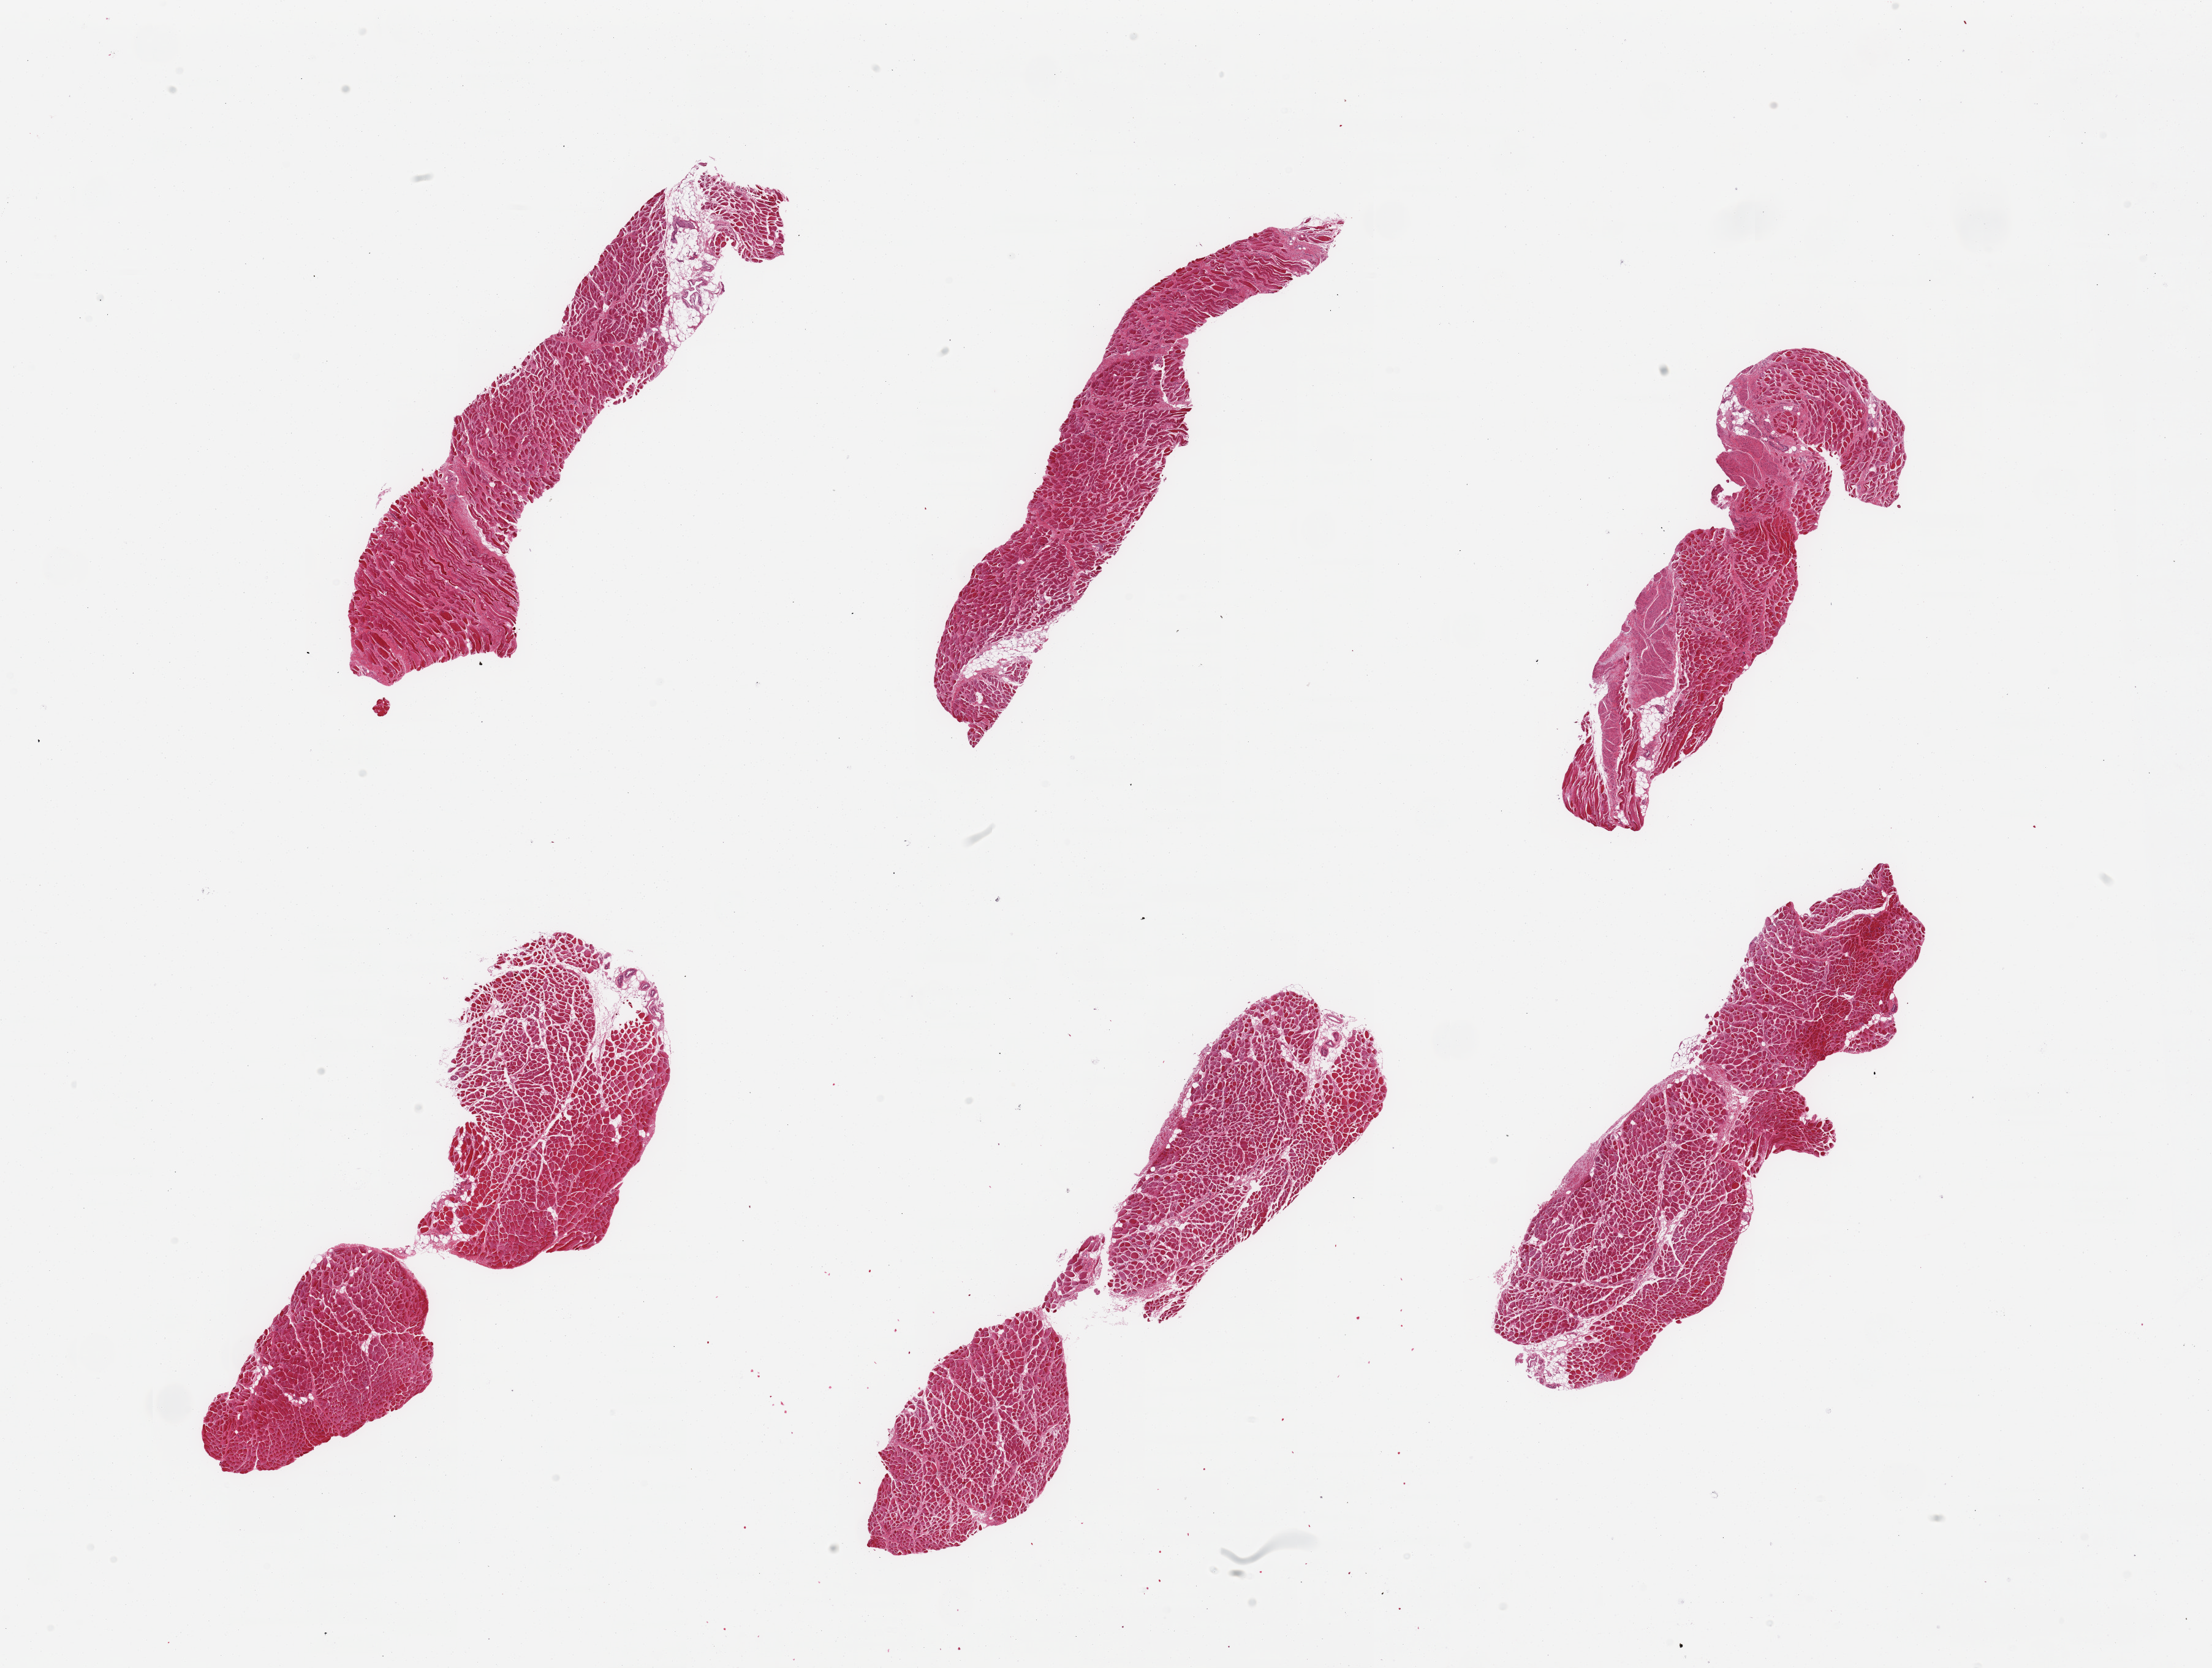
Hematoxylin and eosin (H&E) whole-slide image — low-resolution overview of the scanned area, about 28.5 x 21.5 mm, PAXgene-fixed paraffin-embedded (PFPE) section, section of vagina (target tissue), tissue donor sample. Donor: female.
Review note (as recorded): 6 pieces; mildly to moderately autolyzed skeletal muscle; focal smooth muscle tissue; target vagina not present.